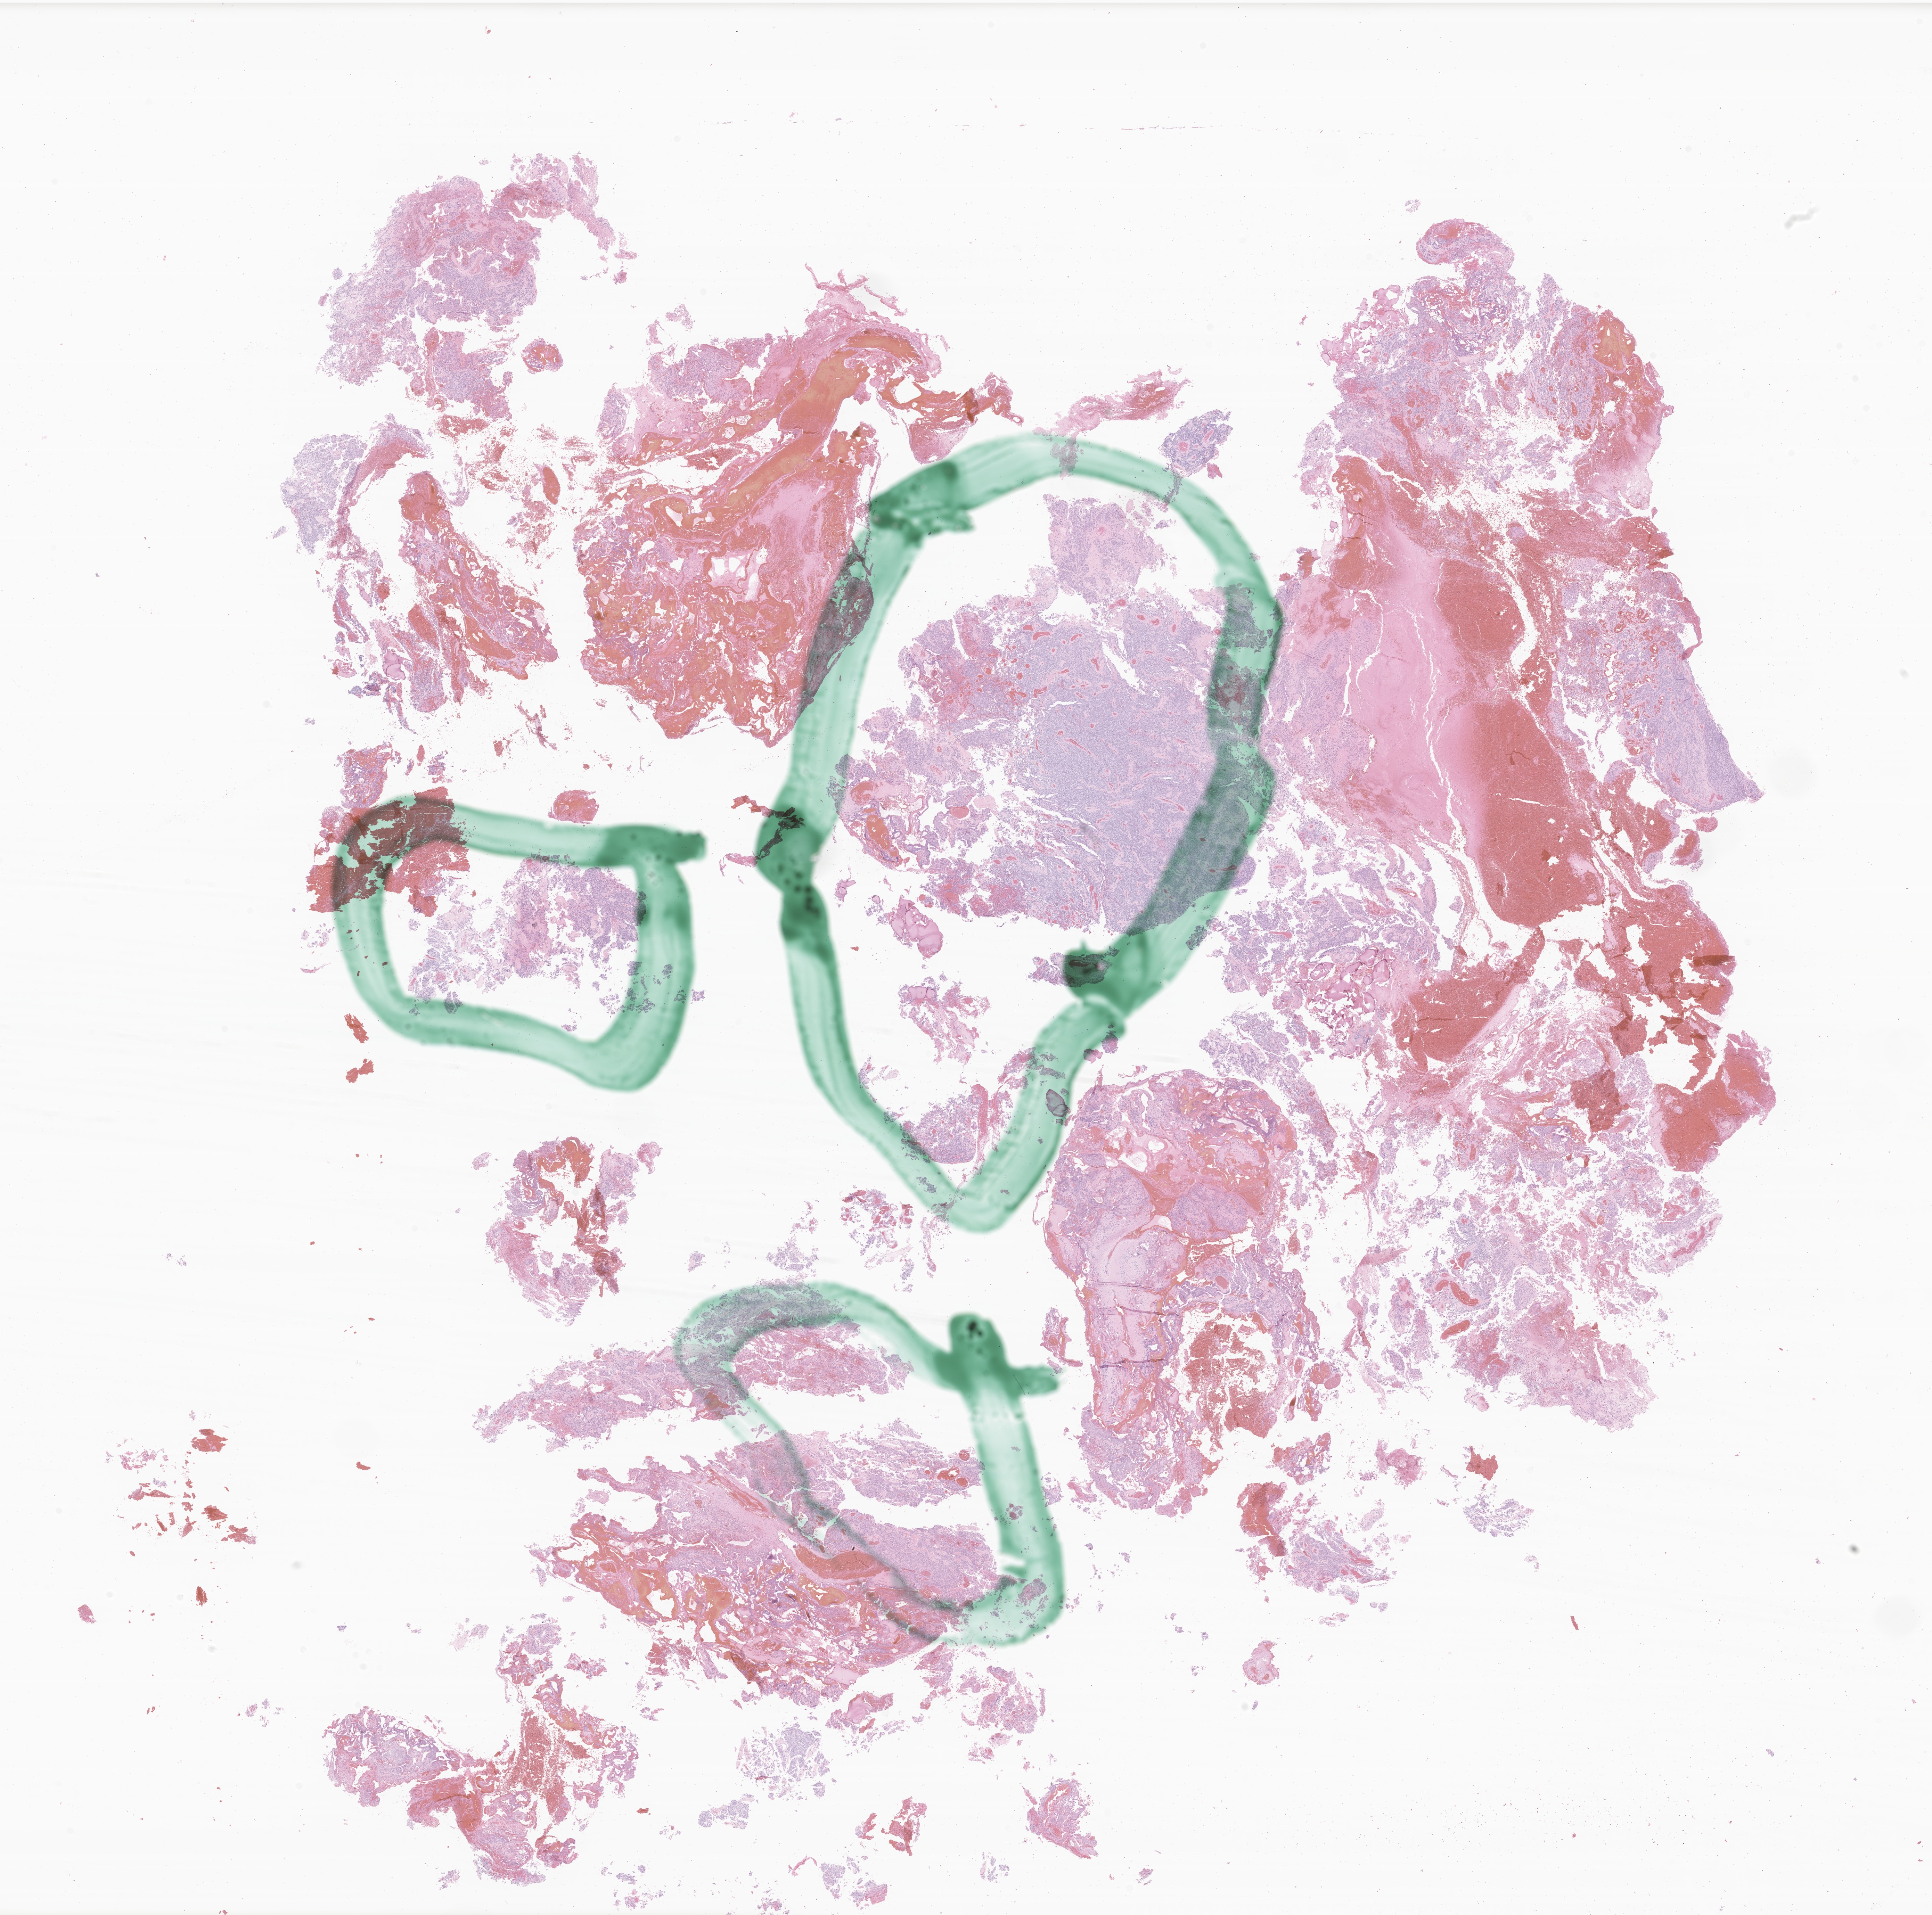
Digitized haematoxylin and eosin-stained section of tumor tissue from the brain — low-resolution overview of the scanned area, about 23.4 x 23.2 mm, formalin-fixed paraffin-embedded section. Patient female; age 87 months (7 years 3 months).
Diagnosis: Ependymoma, anaplastic.